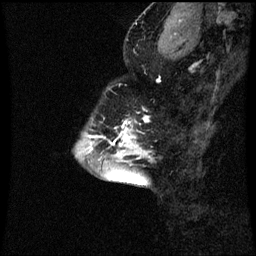
Breast MRI (dynamic contrast-enhanced), one sagittal slice. Slice 20 of 60 in the series (ordered by position). Dynamic contrast-enhanced series, image 2 of 3 at this slice position (ordered by acquisition). 1.5 T. TE 4.2 ms, TR 8.9 ms. 256 × 256 image matrix, field of view 200 × 200 mm. Patient: female, 43 years. From the clinical record (not read from this slice): setting: breast cancer imaged before/during neoadjuvant chemotherapy; receptor status: HR-positive, HER2-negative.
Outlined on this slice (semi-automatic segmentation, software-assisted and operator-edited):
- analysis volume of interest (the breast-tissue region the enhancement analysis was run in; not a lesion): bounding box <96,110,153,159> (left, top, right, bottom; pixels)
- tumour enhancement mask (voxels above the 70 % enhancement threshold inside the analysis volume of interest): <118,118,149,155>